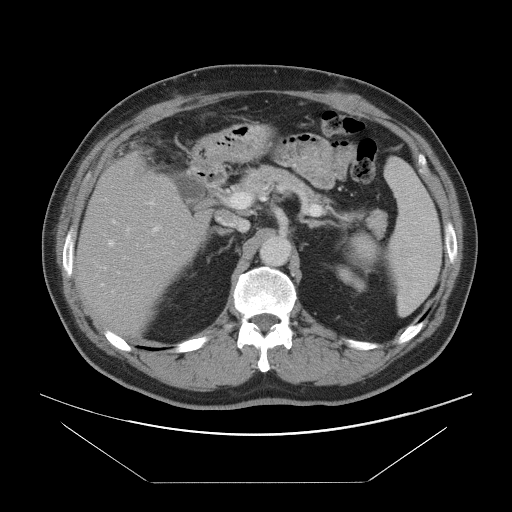
Contrast-enhanced abdominal CT, one axial slice; slice 52 of 97 in the series (ordered by position); 120 kVp; intravenous contrast given; soft-tissue window (W 400 / L 40 HU); 512 × 512 image matrix. Male patient, age 62 years. Case-level facts recorded for this patient, not image findings: diagnosis: colorectal cancer liver metastases, imaged before liver resection; multiple liver metastases: no; largest metastasis: 7 cm.
Structures marked on this image (expert manual segmentation):
- hepatic veins: bounding box [x1, y1, x2, y2] px = [108, 228, 175, 259]
- liver: [77, 155, 206, 335]
- planned liver remnant (the part of the liver to remain after resection): [77, 175, 206, 336]
- portal vein (with intrahepatic branches): [113, 202, 160, 272]
- liver metastasis: [144, 170, 149, 177]